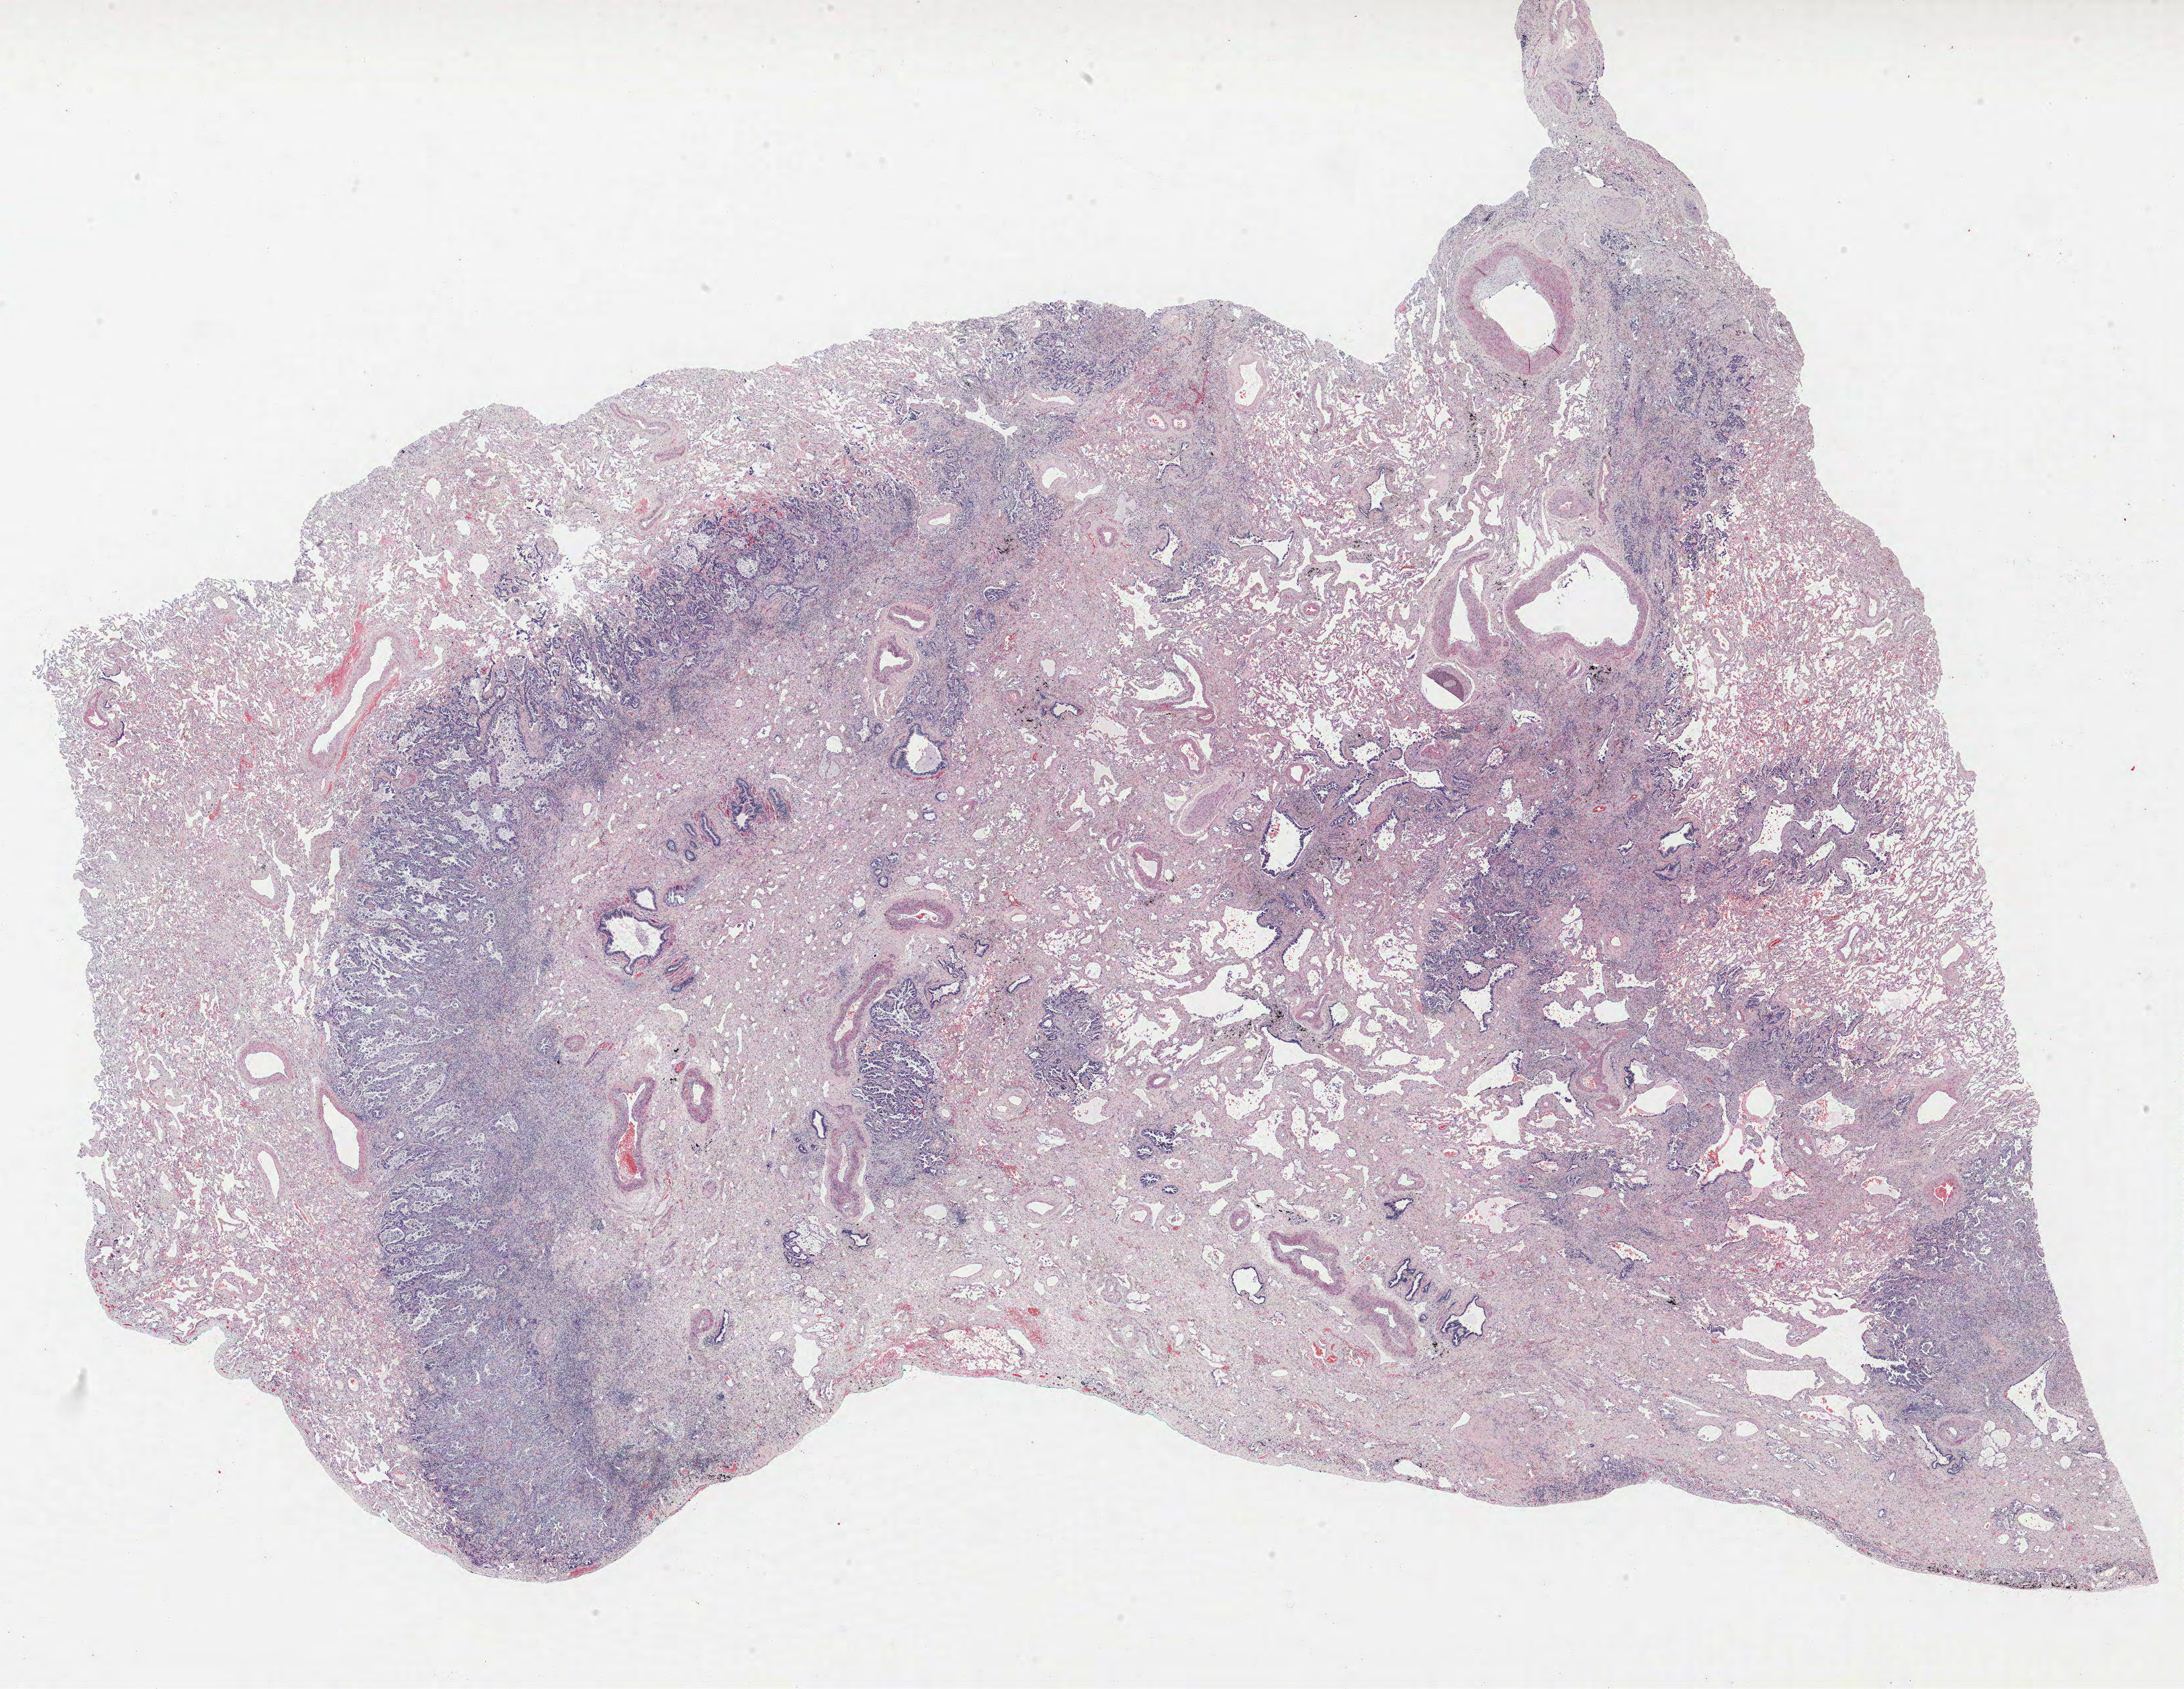
H&E whole-slide image, shown as a low-resolution overview of the whole scanned area (about 26.4 x 20.4 mm, acquisition: 40x scan). FFPE section. Lung. Female, age 68 at enrolment. Former smoker at enrolment. Grade: poorly differentiated (G3).
Participant's lung-cancer diagnosis: Adenocarcinoma, NOS. Primary tumour location (clinical record): left upper lobe. Tumour size (pathology): 50 mm. Stage (AJCC 6th edition): IB.